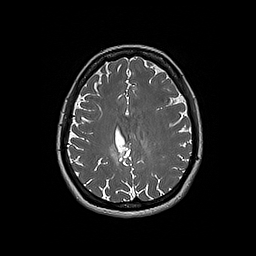
Brain MRI from a brain-tumour surgery series, one axial slice; slice 70 of 192 in the series (ordered by position); 256 × 256 image matrix, field of view 250 × 250 mm. From the clinical record (not read from this slice): histopathology: Oligodendroglioma; WHO grade: 2; IDH mutation: yes; tumour location: Right Parietal.
Structures marked on this image (outlined manually by an expert reader):
- tumour: bounding box [x1, y1, x2, y2] px = [110, 145, 124, 164]